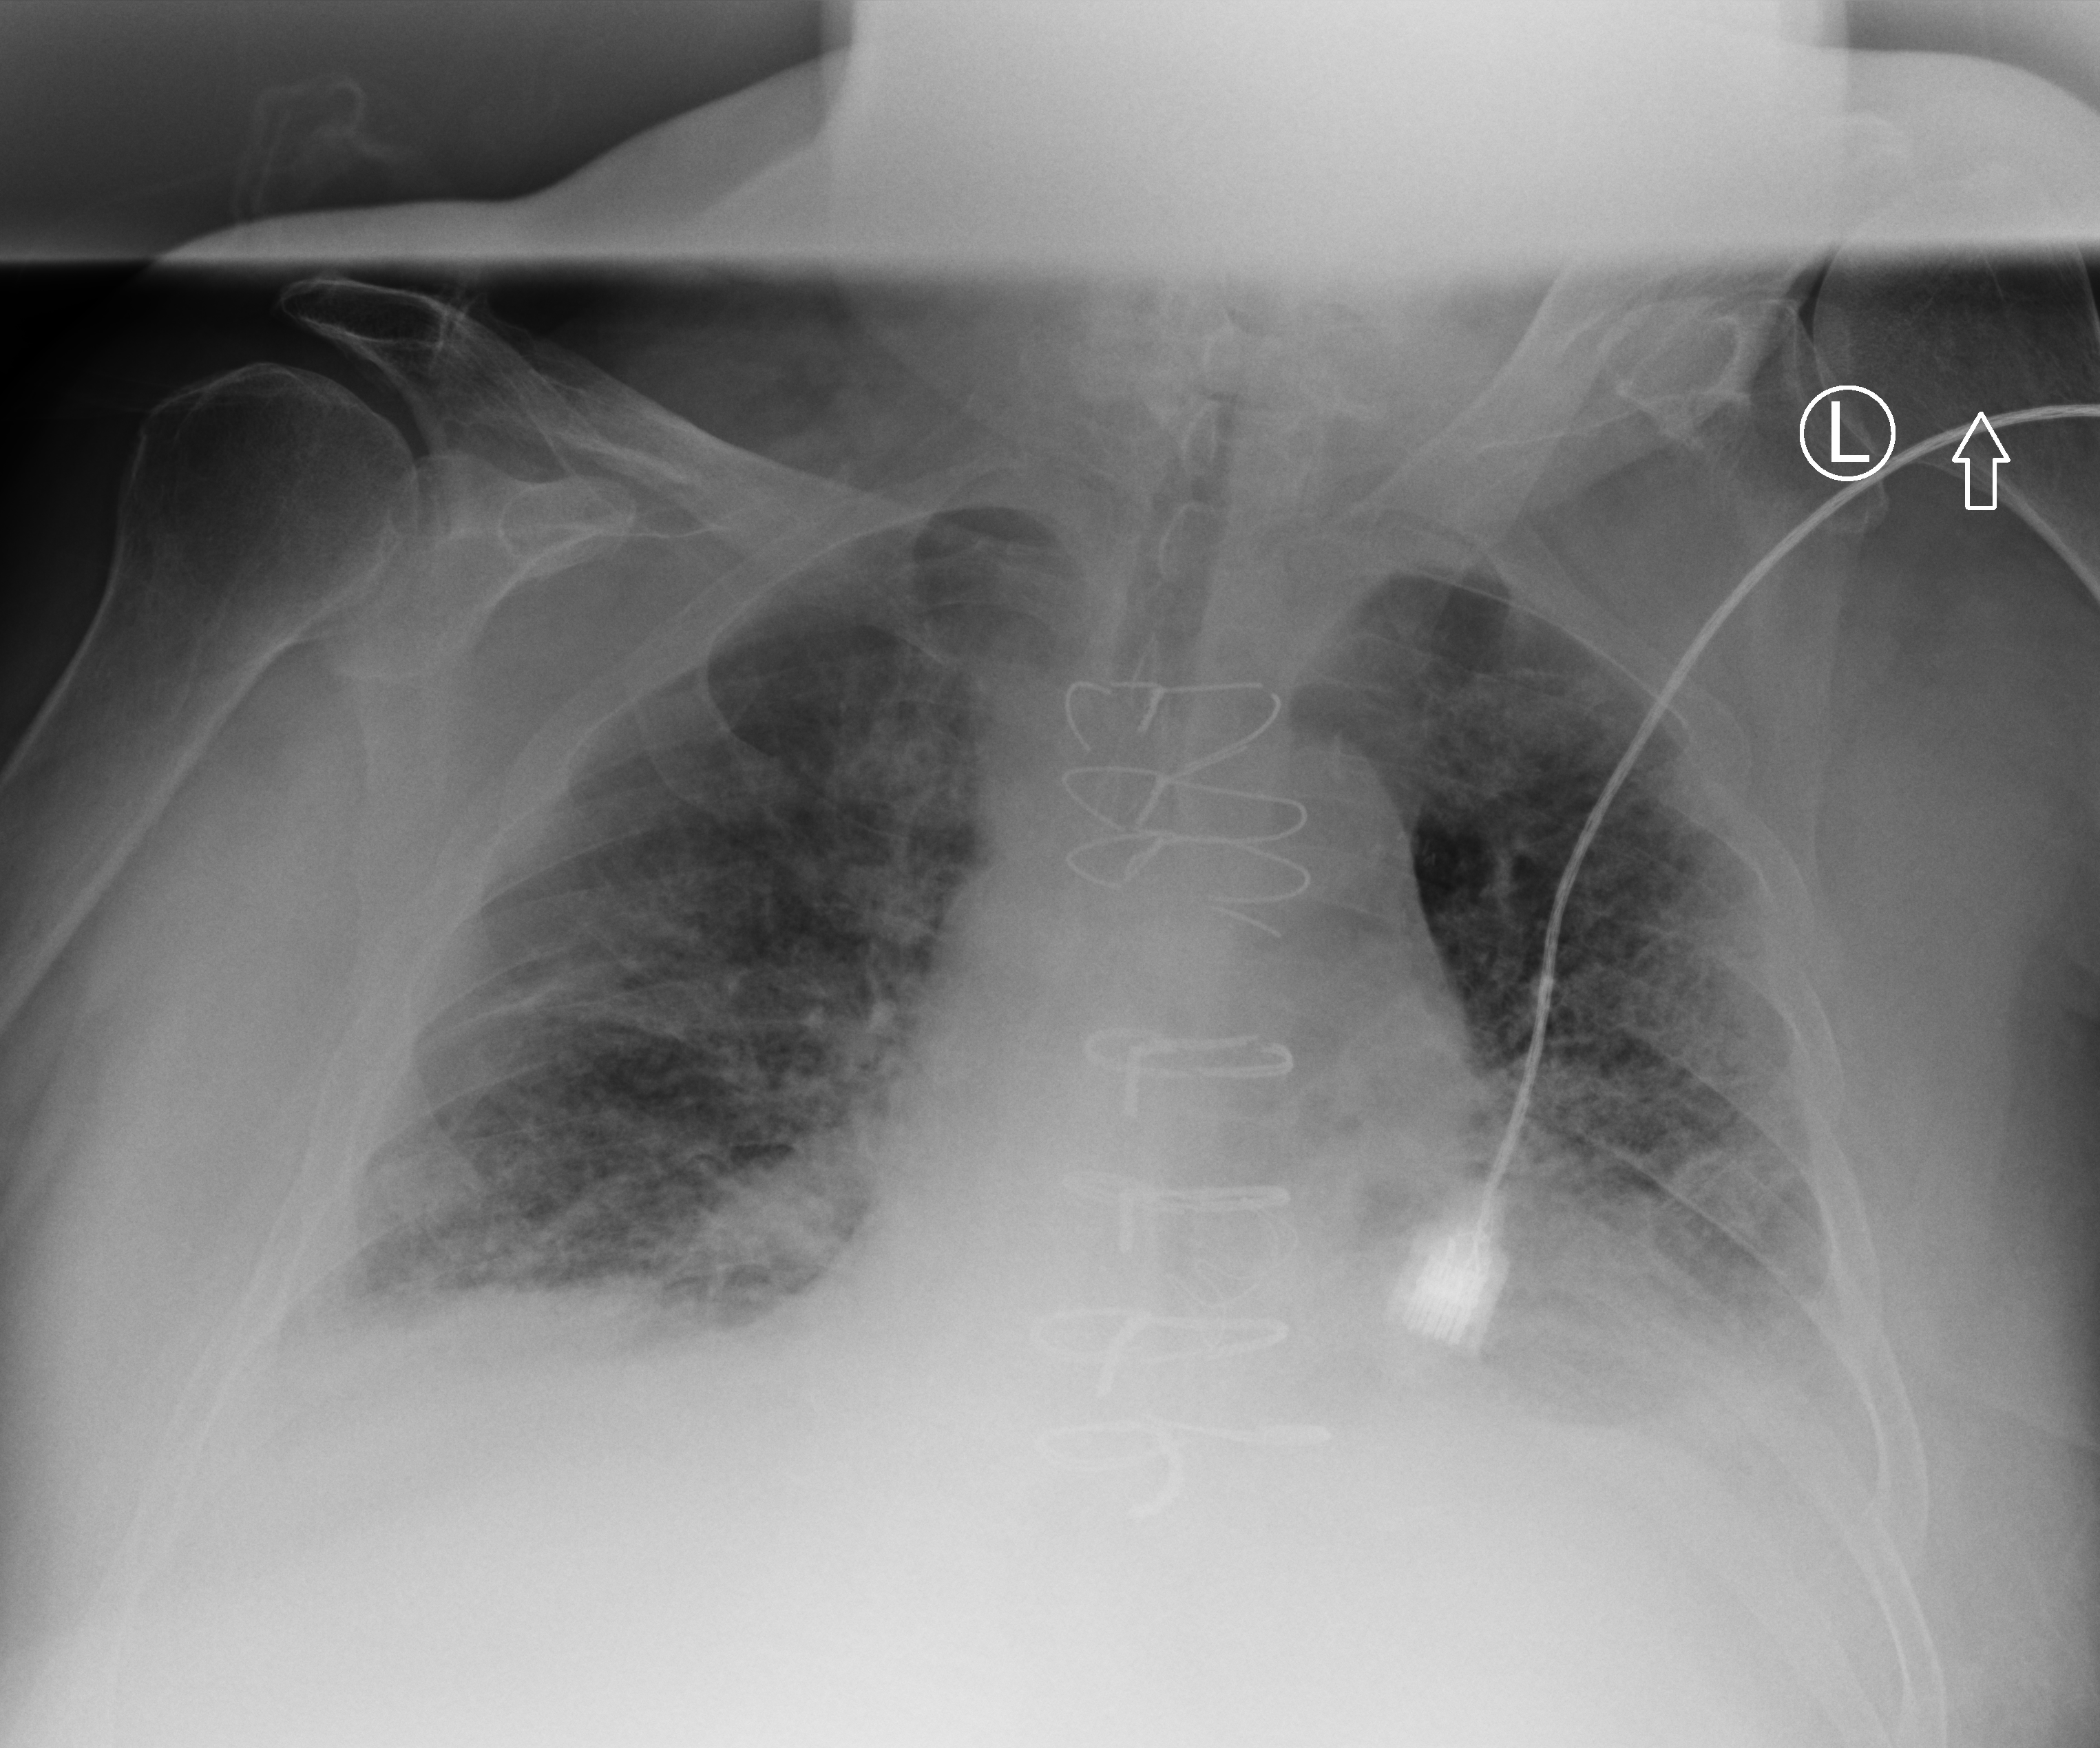
Portable chest radiograph, anteroposterior (AP) projection. Patient hospitalised with COVID-19; male, aged 75–90 years.
Admission-level facts for this patient (not findings on this image; timing relative to this image not recorded): admitted to intensive care during this hospital stay: no; mechanically ventilated during this hospital stay: no.